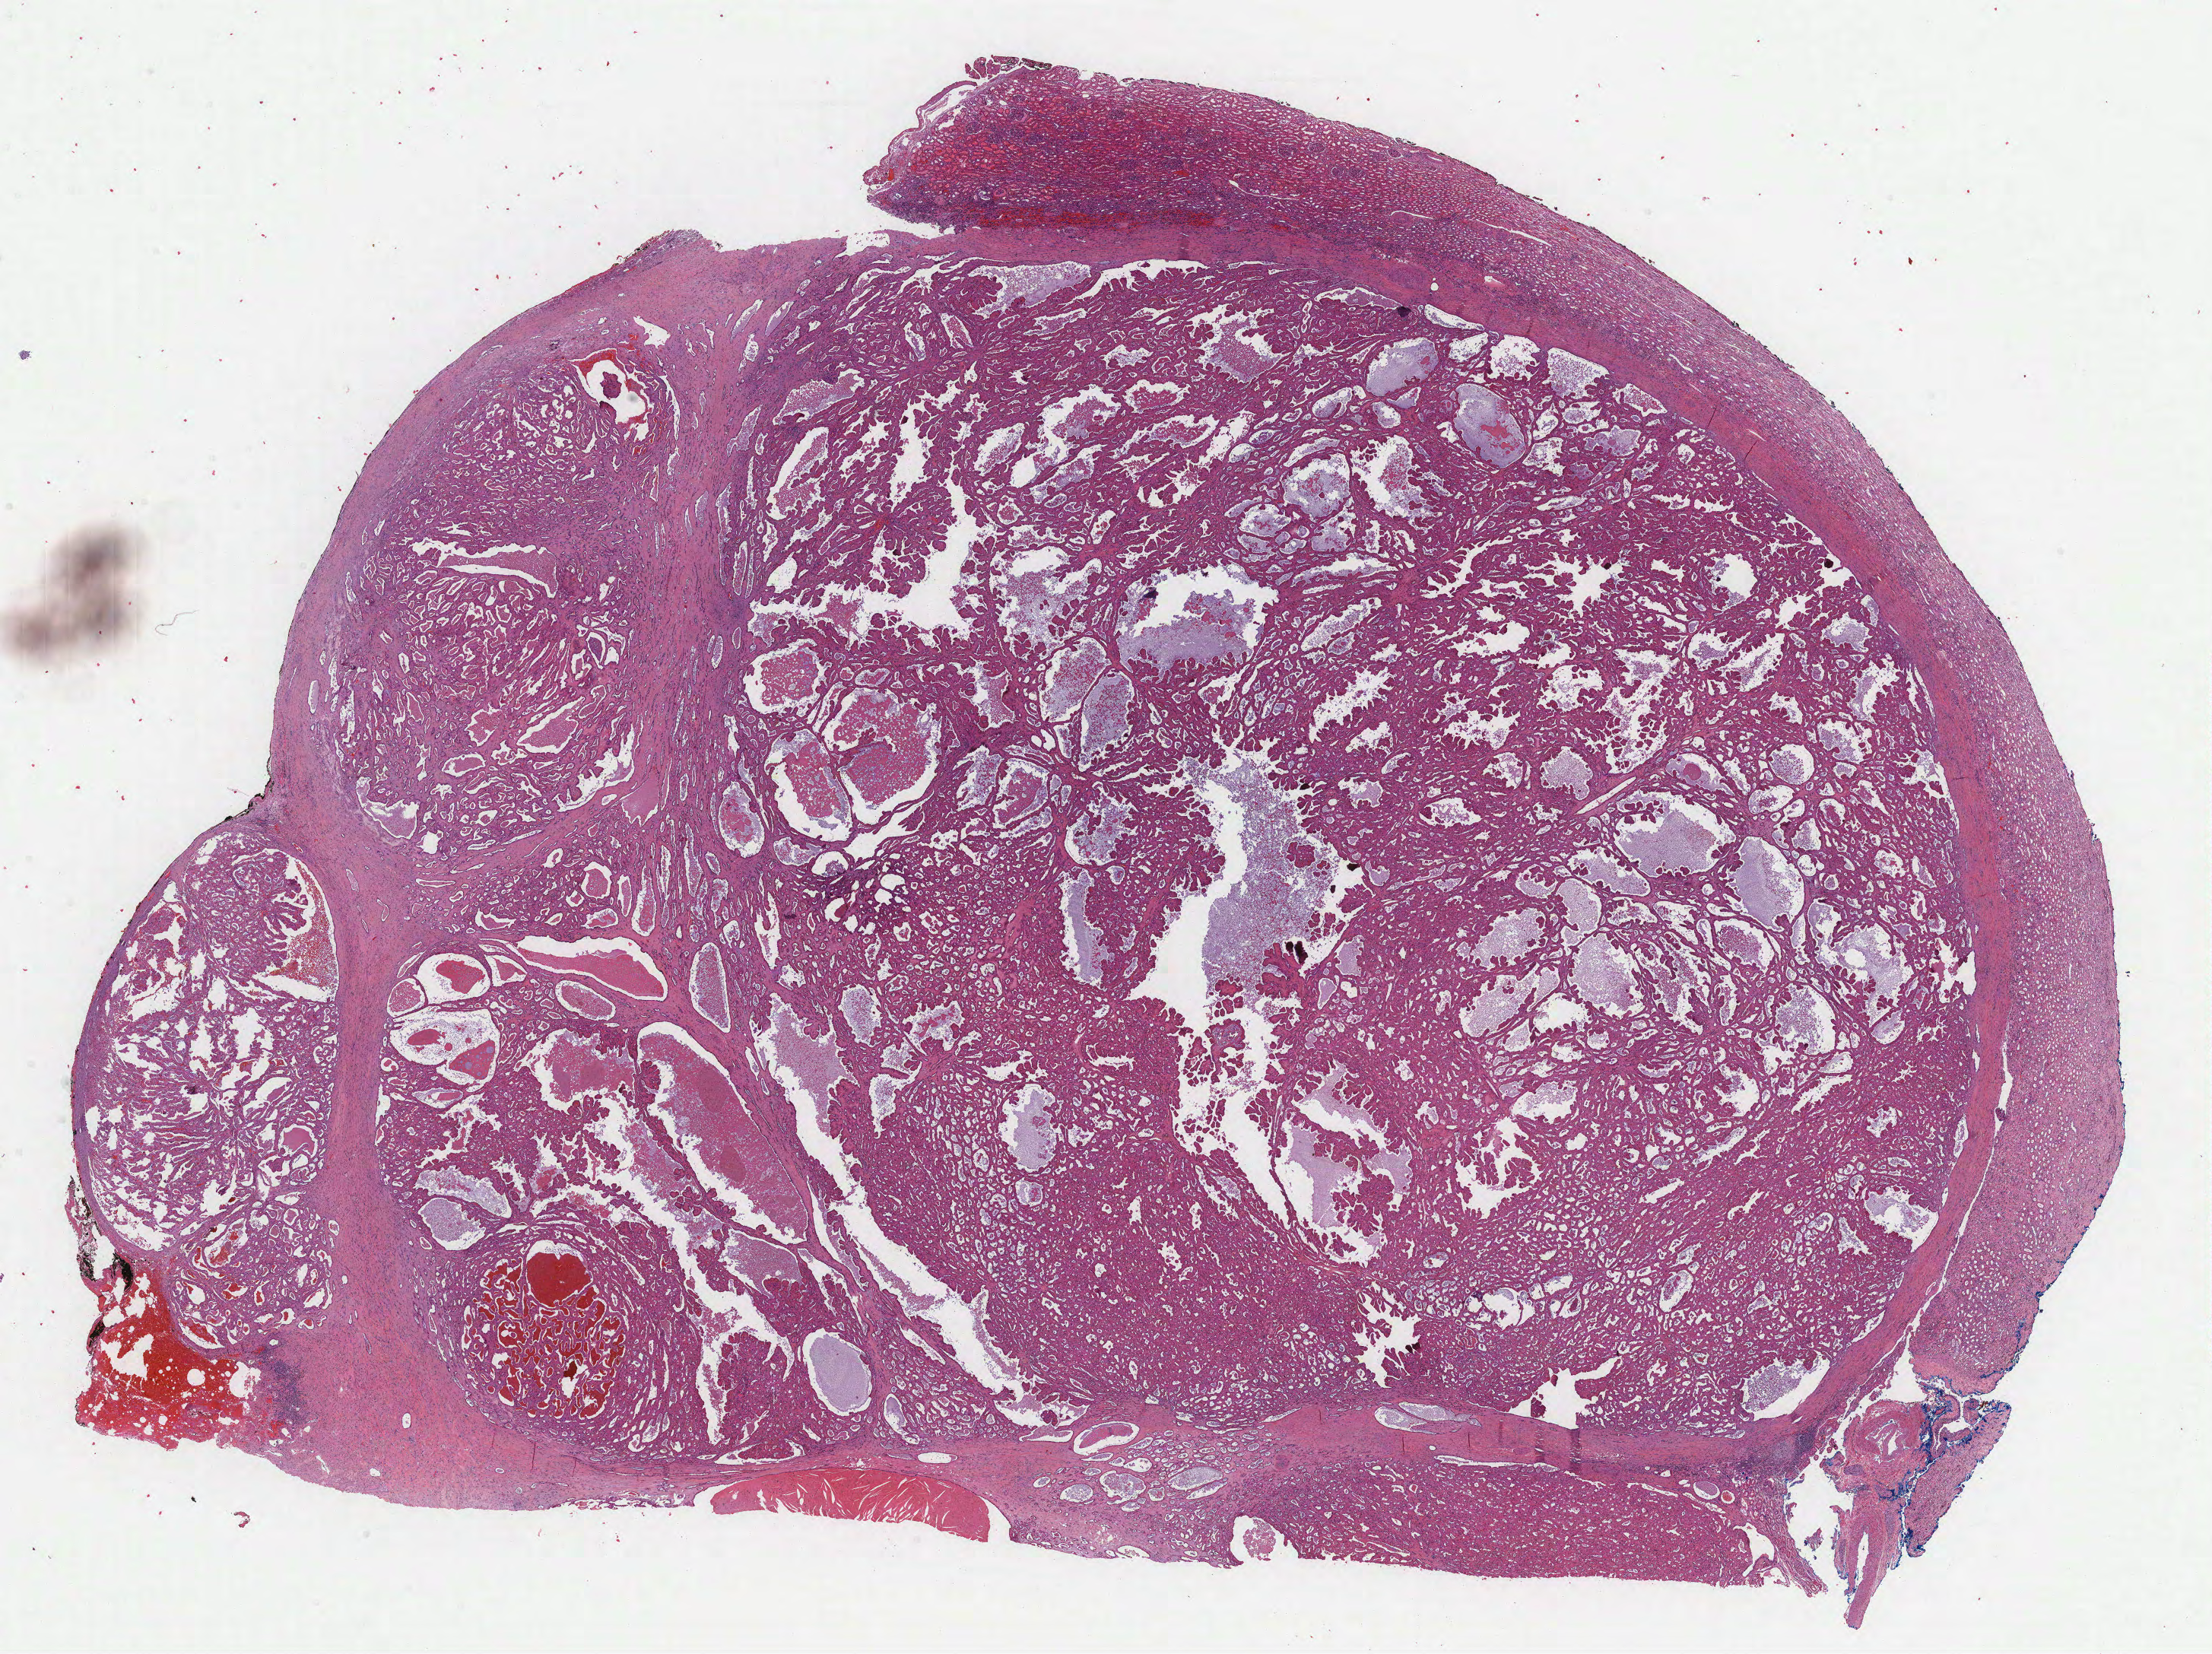
Digitized H&E tissue section (whole slide) — whole scanned area (about 23.5 x 17.6 mm) shown as a low-resolution overview. FFPE section. Sample: primary tumour, kidney. Patient: female, age at initial diagnosis 50 years.
Diagnosis: Papillary adenocarcinoma, NOS. AJCC pathologic stage: I (7th edition). TNM: T1a NX MX.